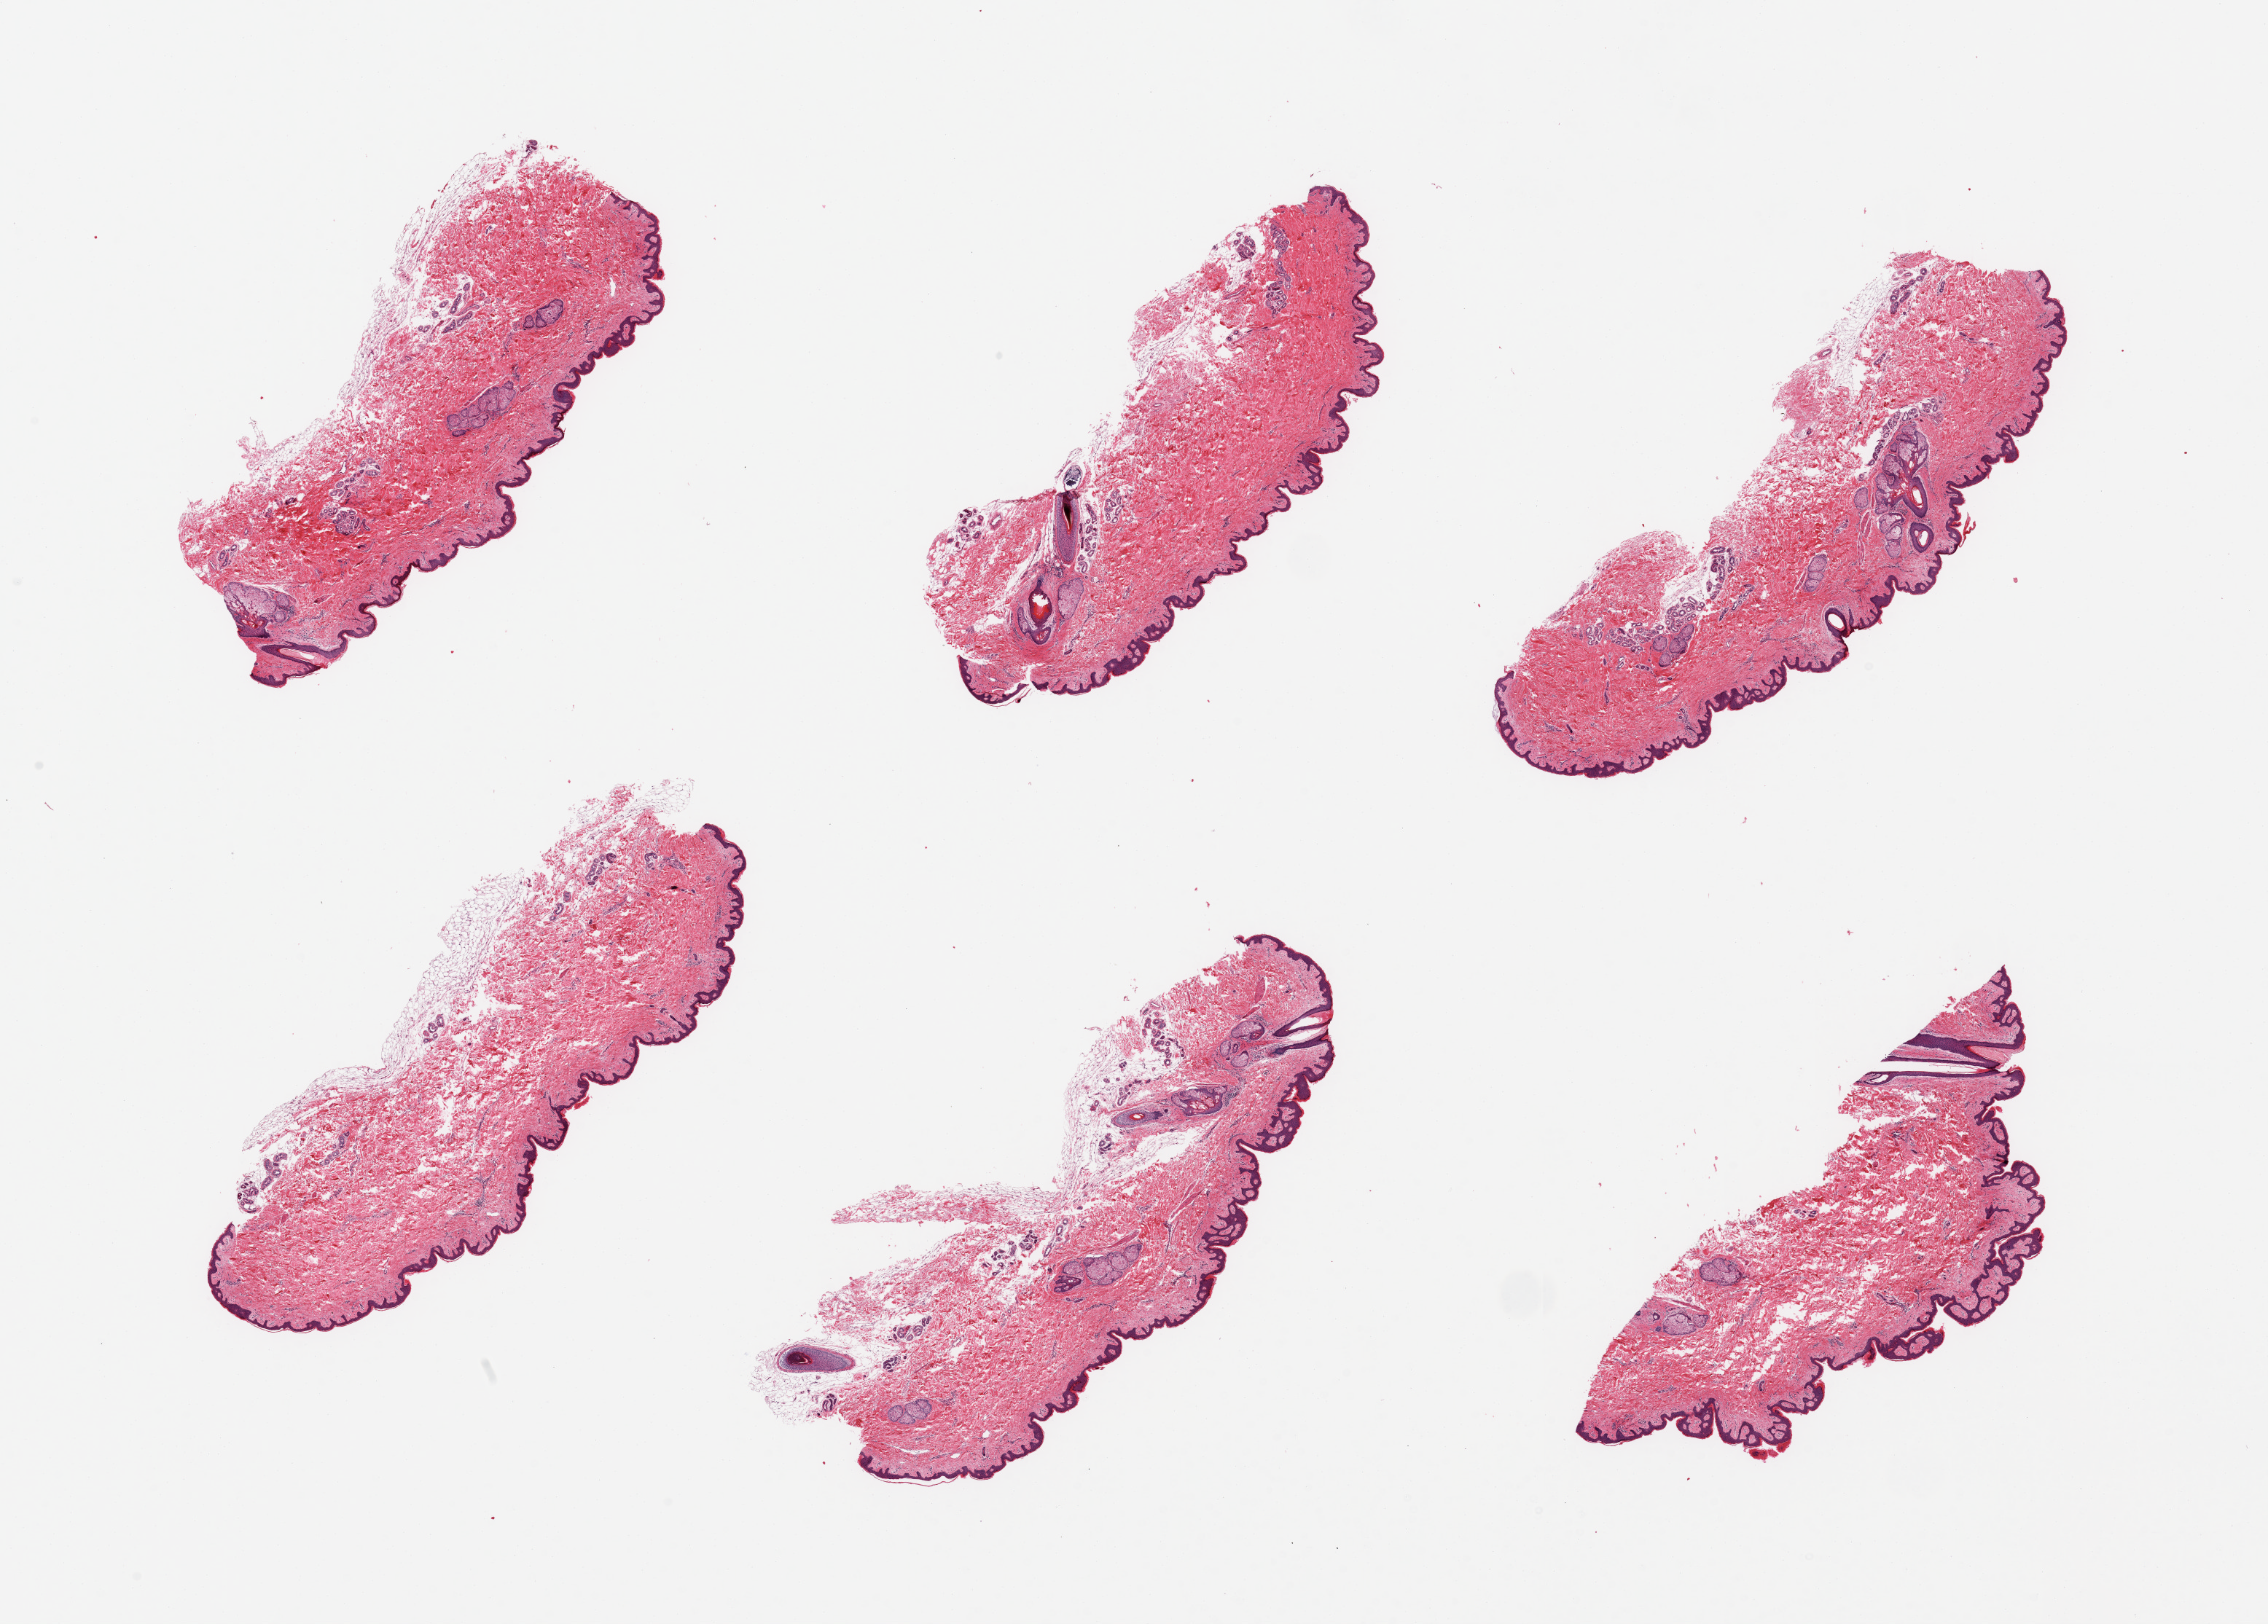
Whole-slide image, H&E stain, brightfield, a low-resolution overview of the entire scanned area, about 24.6 x 17.6 mm. PAXgene-fixed, paraffin-embedded tissue. Sampled site (target tissue): skin of suprapubic region. Tissue donor sample.
Pathologist's review note for this sample: 6 pieces; 5% dermal fat; prominent sebaceous glands and hair follicles in some areas.